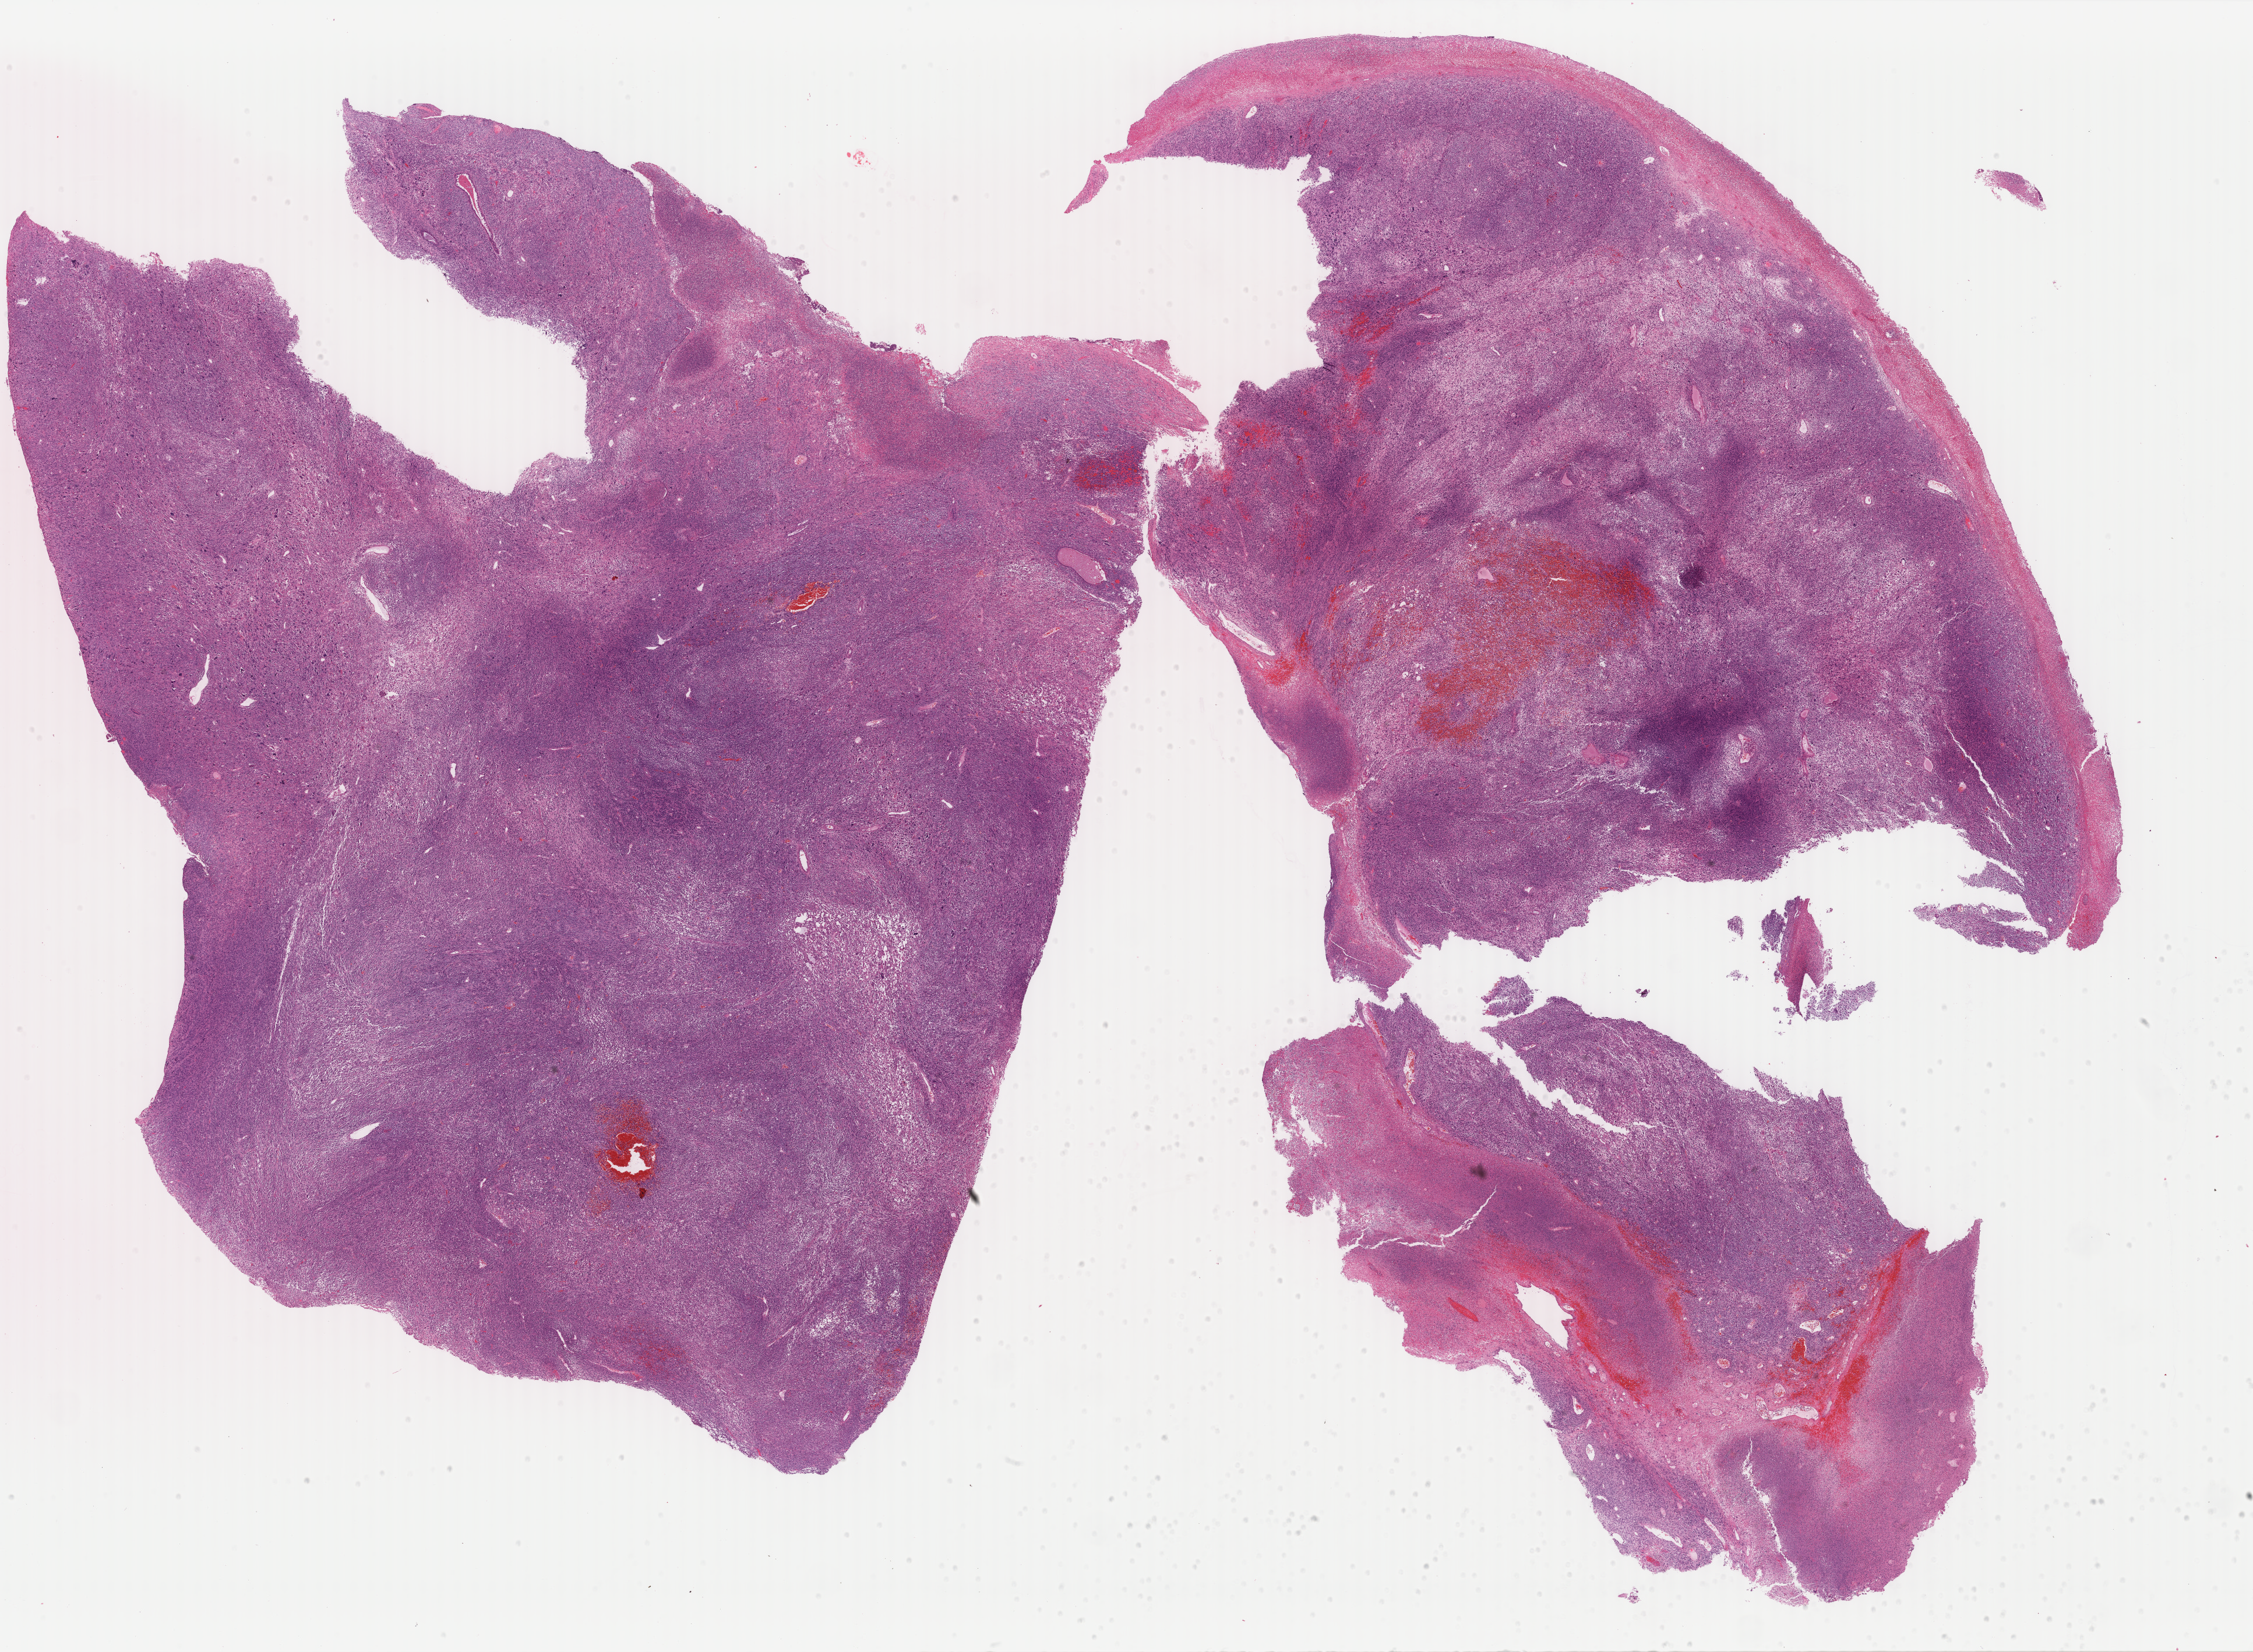
Whole-slide histology image, Hematoxylin and eosin (H&E) stained, low-resolution overview of the scanned area, about 30.7 x 22.5 mm (from a 40x scan), FFPE section, primary tumour sample from the uterus. Female, age 77 years at initial diagnosis.
FIGO stage: IIIA. Histologic diagnosis: Mullerian mixed tumor (fundus uteri).